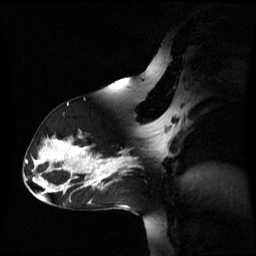
Breast MRI (dynamic contrast-enhanced), one sagittal slice. Slice 37 of 60 in the series (ordered by position). Dynamic contrast-enhanced series, image 2 of 3 at this slice position (ordered by acquisition). 1.5 T. TE 4.2 ms, TR 8.4 ms. 256 × 256 image matrix, field of view 270 × 270 mm. Patient: female, 39 years. Case-level facts recorded for this patient, not image findings: setting: breast cancer imaged before/during neoadjuvant chemotherapy; receptor status: triple-negative.
Structures marked on this image (semi-automatically segmented with operator editing):
- analysis volume of interest (the breast-tissue region the enhancement analysis was run in; not a lesion): bounding box [x1, y1, x2, y2] px = [105, 149, 148, 178]
- tumour enhancement mask (voxels above the 70 % enhancement threshold inside the analysis volume of interest): [105, 157, 125, 176]